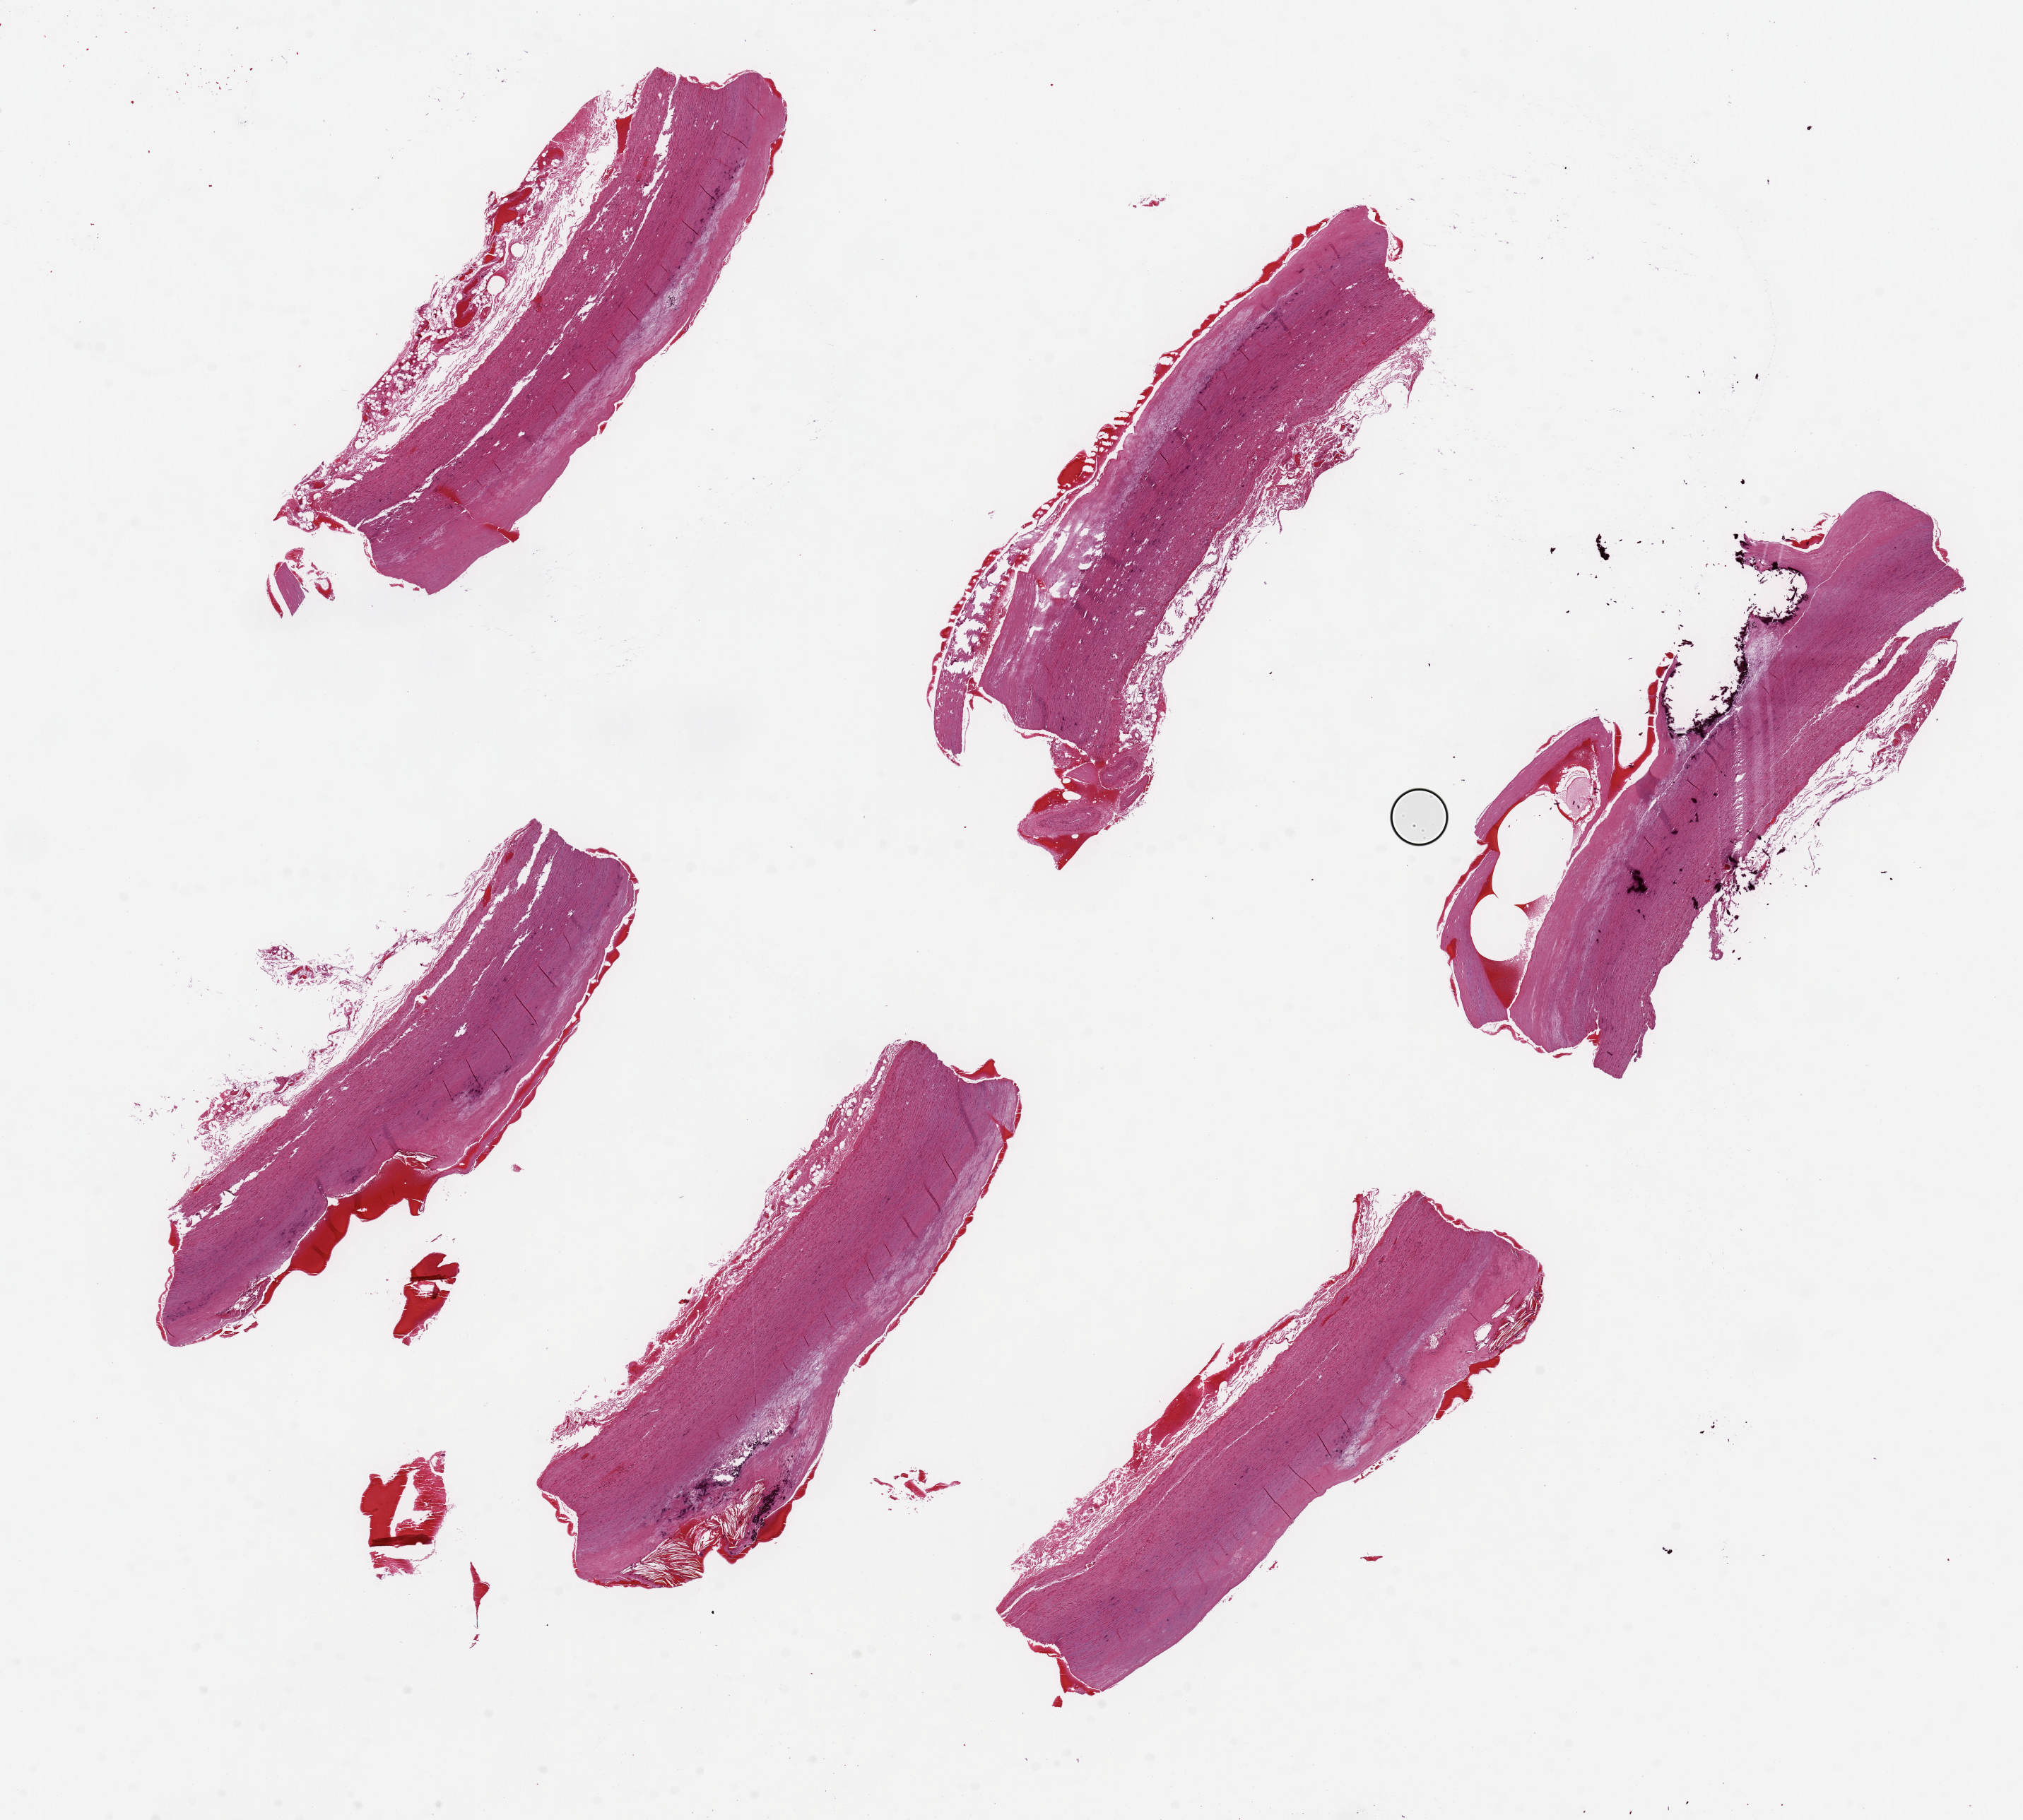
Digitized hematoxylin and eosin (H&E)-stained section, brightfield, a low-resolution overview of the entire scanned area, about 22.6 x 20.4 mm (from a 20x scan); PAXgene-fixed paraffin-embedded (PFPE) section; target tissue: aorta; tissue donor sample. Male donor.
Review note (as recorded): 6 pieces, up to 8x3mm; calcified plaques.